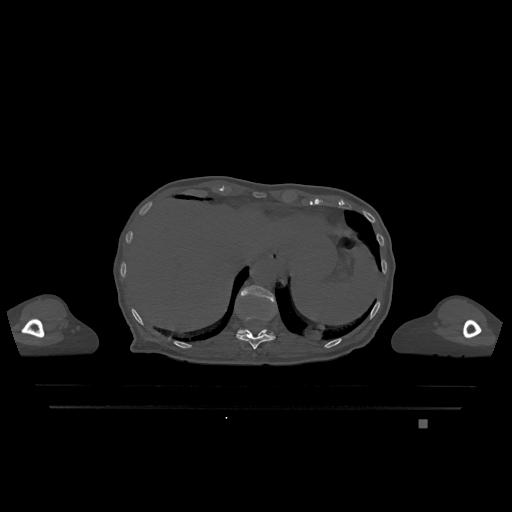
CT including the spine, one axial slice. Slice 573 of 1317 in the series (ordered by position). Bone window (W 1800 / L 400 HU). 0.5 mm slice thickness. 512 × 512 image matrix, field of view 500 × 500 mm. Patient: female, 74 years. From the clinical record (not read from this slice): primary cancer: lung.
Outlined on this slice (semi-automatic segmentation, software-assisted and operator-edited):
- T11 vertebra: box from (x=236, y=316) to (x=276, y=349) px
- T12 vertebra: (x=238, y=285)–(x=276, y=336)